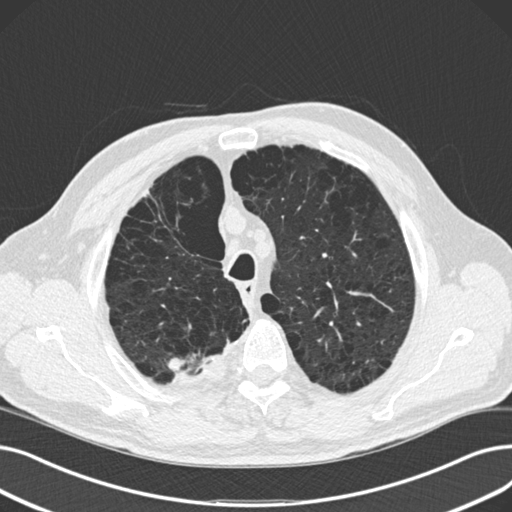
Low-dose screening chest CT, one axial slice. Position 124 of 165 along the scan axis. 120 kVp. Lung window (W 1500 / L -600 HU). 512 × 512 image matrix, field of view 369 × 369 mm.
Structures marked on this image (manually delineated by an expert):
- lesion 2 (tumor, upper lobe of right lung): bounding box (x1, y1, x2, y2) in pixels: (168, 358, 183, 372)